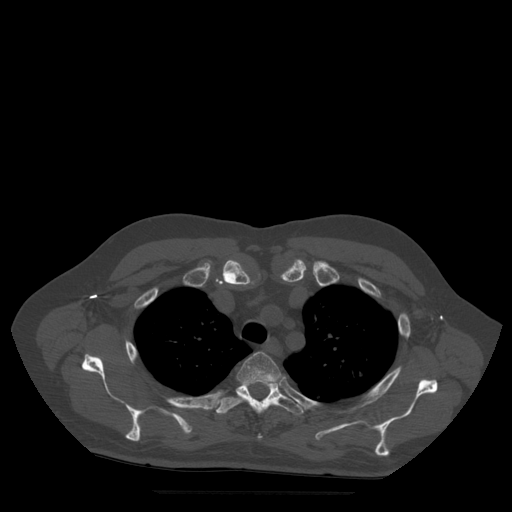
CT including the spine, one axial slice. Position 399 of 522 along the scan axis. Bone window (W 1800 / L 400 HU). 512 × 512 image matrix, field of view 420 × 420 mm. Patient age 72 years. From the clinical record (not read from this slice): primary cancer: prostate.
Annotated regions visible in this slice (semi-automatically segmented with operator editing):
- T3 vertebra: box from (x=237, y=352) to (x=282, y=439) px
- T4 vertebra: (x=215, y=383)–(x=304, y=415)